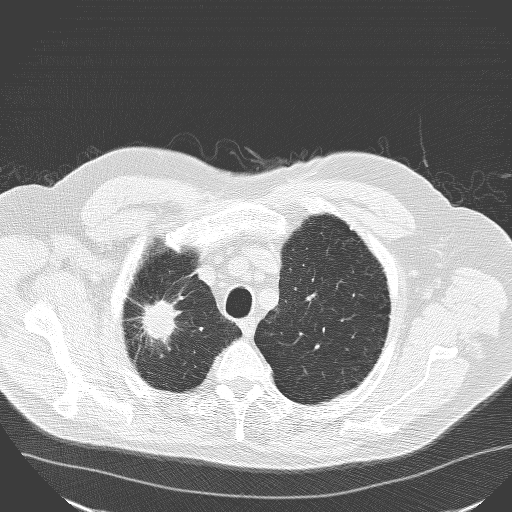
Low-dose screening chest CT, one axial slice; position 137 of 160 along the scan axis; lung window (W 1500 / L -600 HU); 3.2 mm slice thickness; 512 × 512 image matrix, field of view 400 × 400 mm.
Annotated regions visible in this slice (manually delineated by an expert):
- lesion 1 (tumor, upper lobe of right lung): box from (x=140, y=299) to (x=179, y=342) px